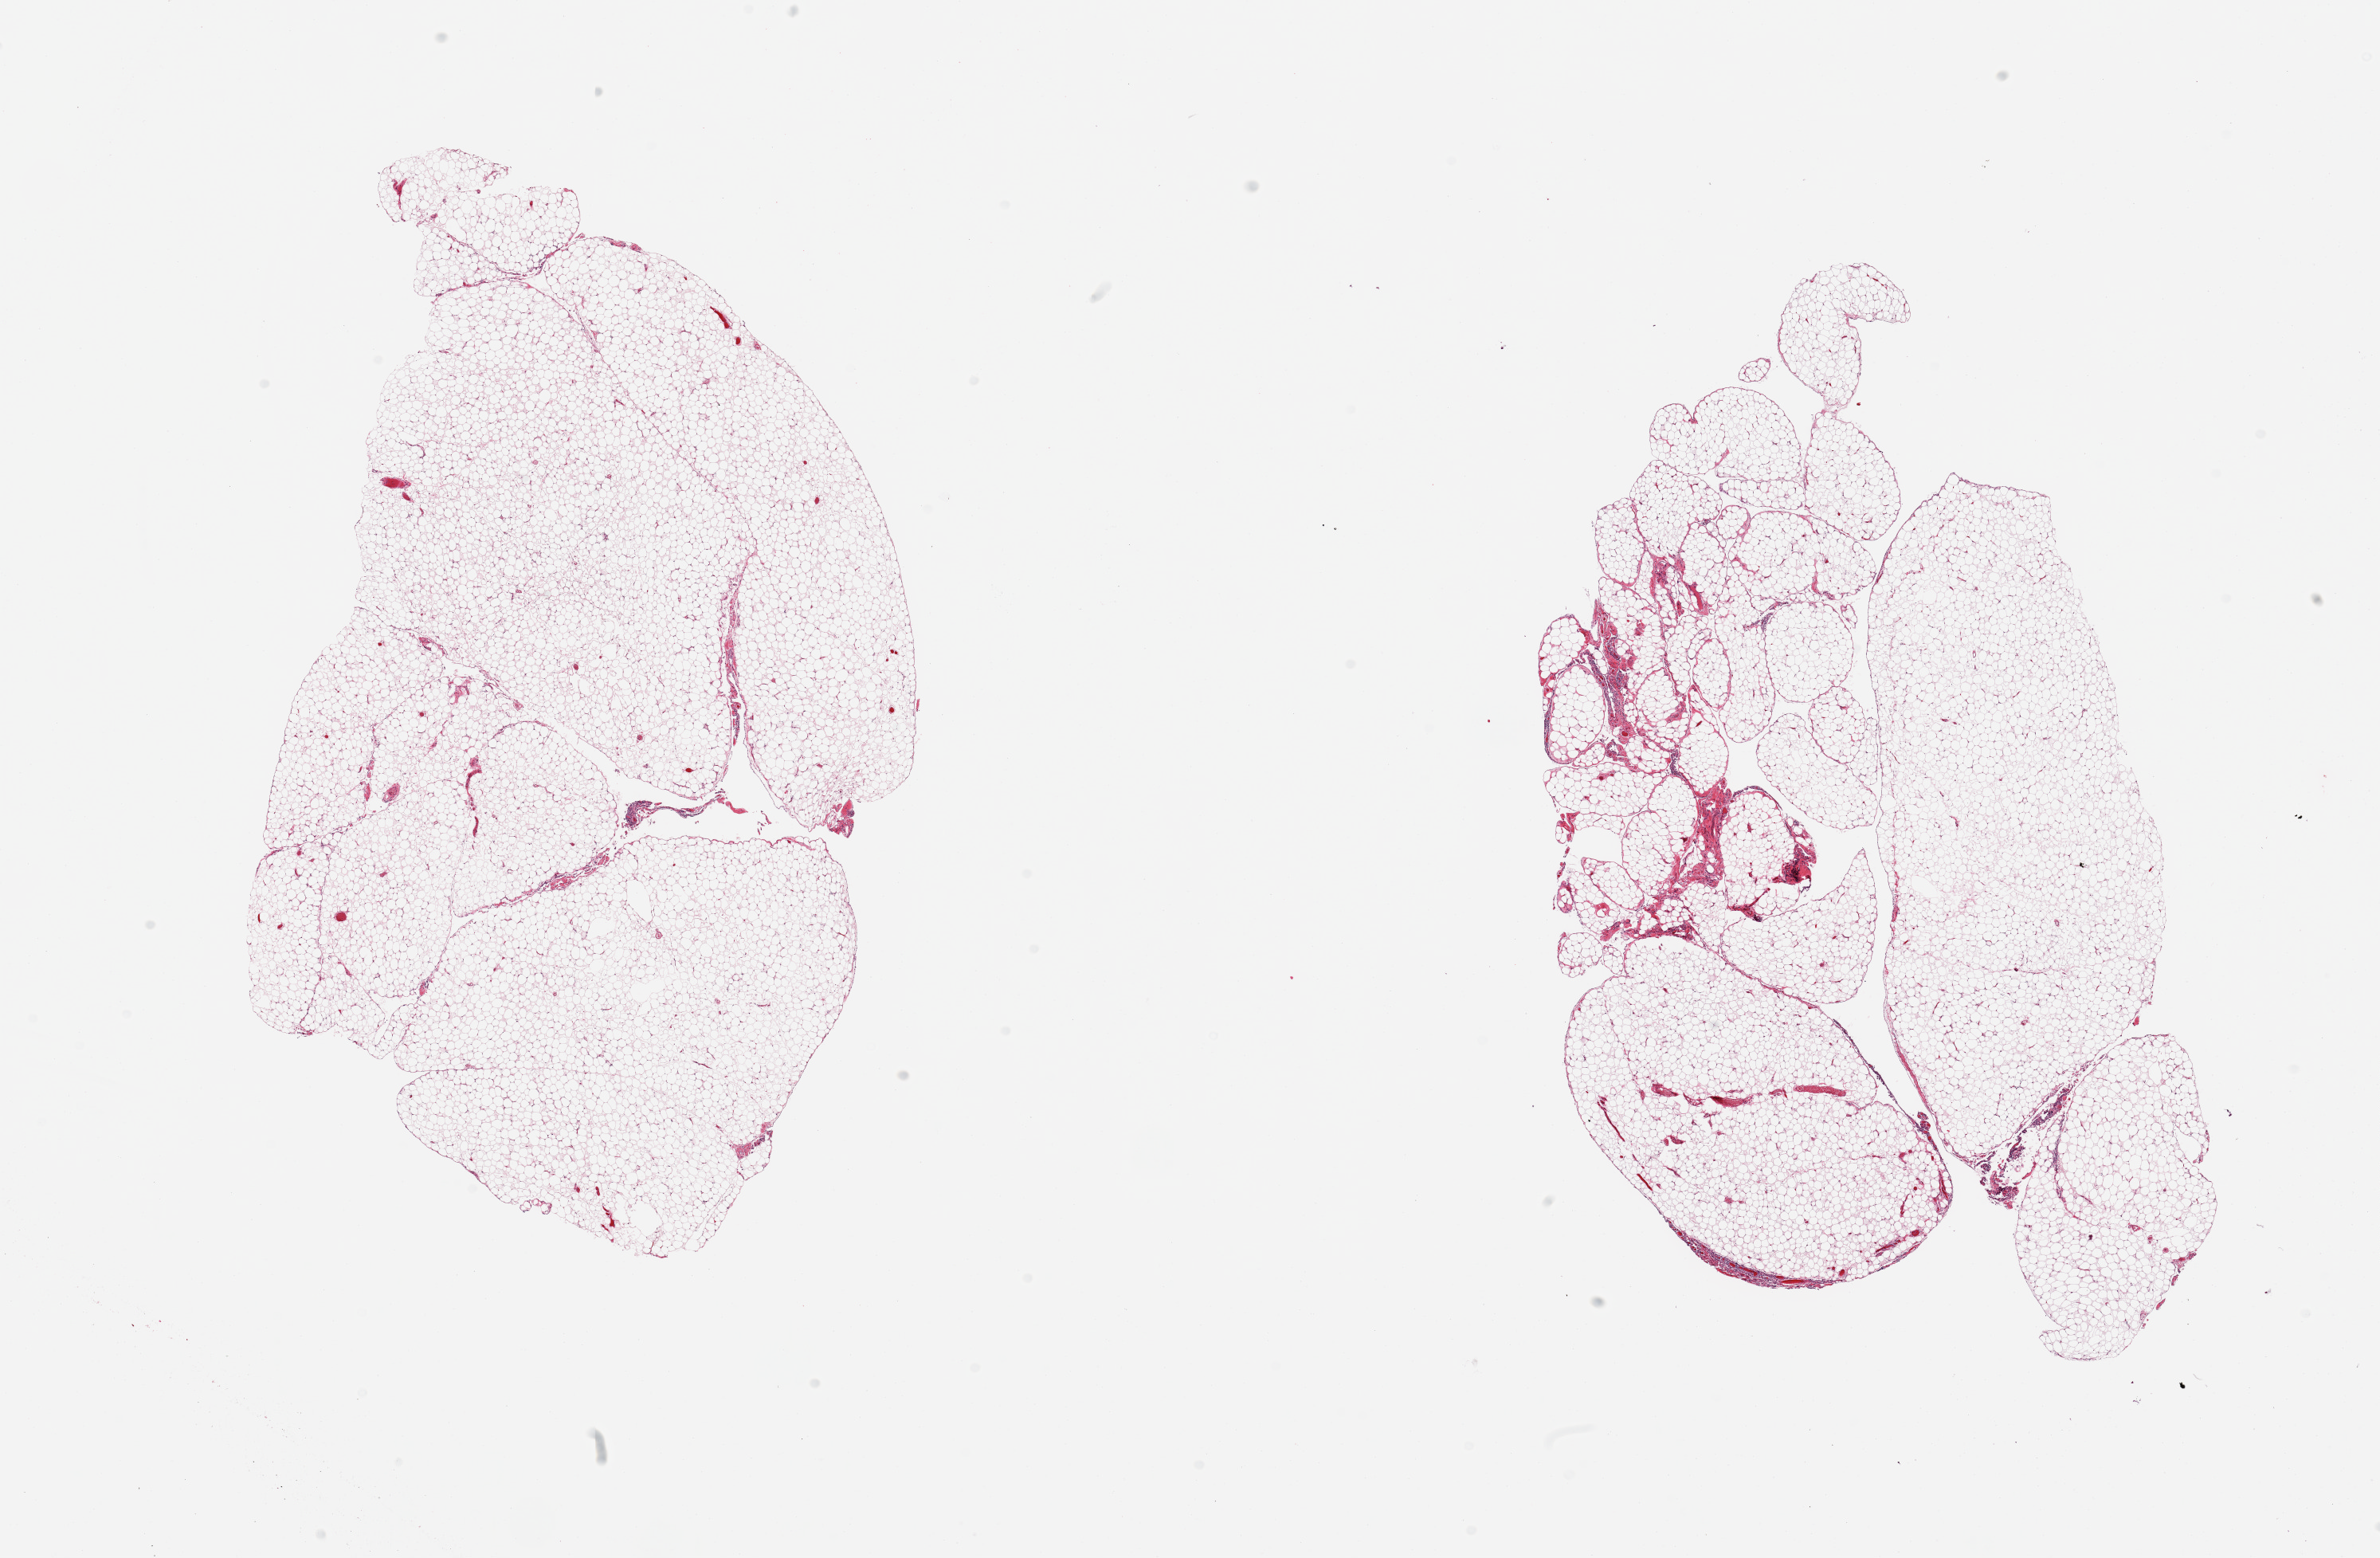
Haematoxylin and eosin whole-slide image, brightfield — low-resolution overview of the scanned area, about 23.6 x 15.5 mm (from a 20x scan). PAXgene-fixed, paraffin-embedded tissue. Sampled site (target tissue): omentum. Tissue donor sample. Donor: male.
Pathologist's review note for this sample: 2 pieces, minimal interstitial fascia/vascular elements.